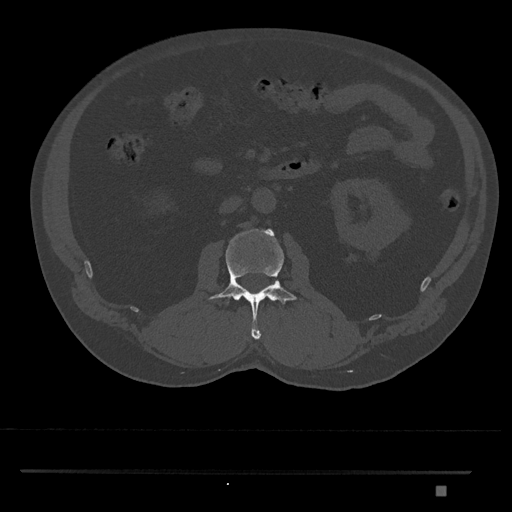
CT including the spine, one axial slice; slice 750 of 1134 in the series (ordered by position); reconstruction kernel Br40s/3; bone window (W 1800 / L 400 HU); 0.5 mm slice thickness; 512 × 512 image matrix. Patient: male, 65 years. Case-level facts recorded for this patient, not image findings: primary cancer: prostate.
Annotated regions visible in this slice (semi-automatically segmented with operator editing):
- L2 vertebra: box from (x=209, y=228) to (x=297, y=340) px